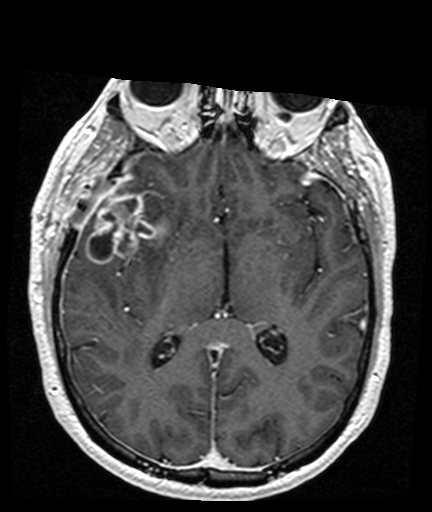
Brain MRI from a brain-tumour surgery series, one axial slice; slice 88 of 176 in the series (ordered by position); T1-weighted post-contrast; 1 mm slice thickness; 432 × 512 image matrix. Case-level facts recorded for this patient, not image findings: histopathology: Glioblastoma; WHO grade: 4; IDH mutation: no; tumour location: Right Frontal Temporal, Posterior Sylvian Fissure.
Structures marked on this image (outlined manually by an expert reader):
- tumour: bounding box [x1, y1, x2, y2] px = [85, 189, 162, 265]